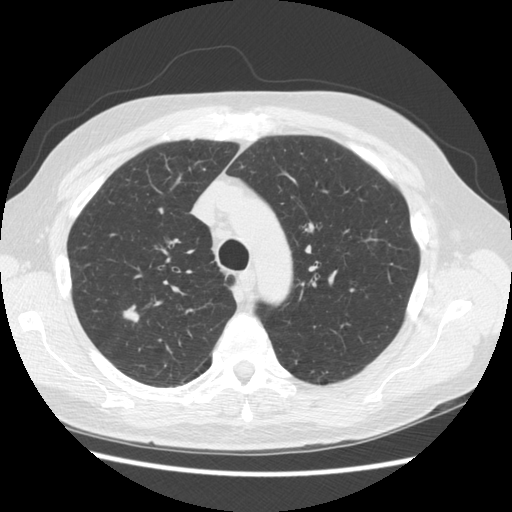
Low-dose screening chest CT, one axial slice. Position 115 of 156 along the scan axis. 140 kVp. Lung window (W 1500 / L -600 HU). 512 × 512 image matrix, field of view 360 × 360 mm.
Annotated regions visible in this slice (manually delineated by an expert):
- lesion 1 (tumor, upper lobe of right lung): bounding box <123,302,139,323> (left, top, right, bottom; pixels)